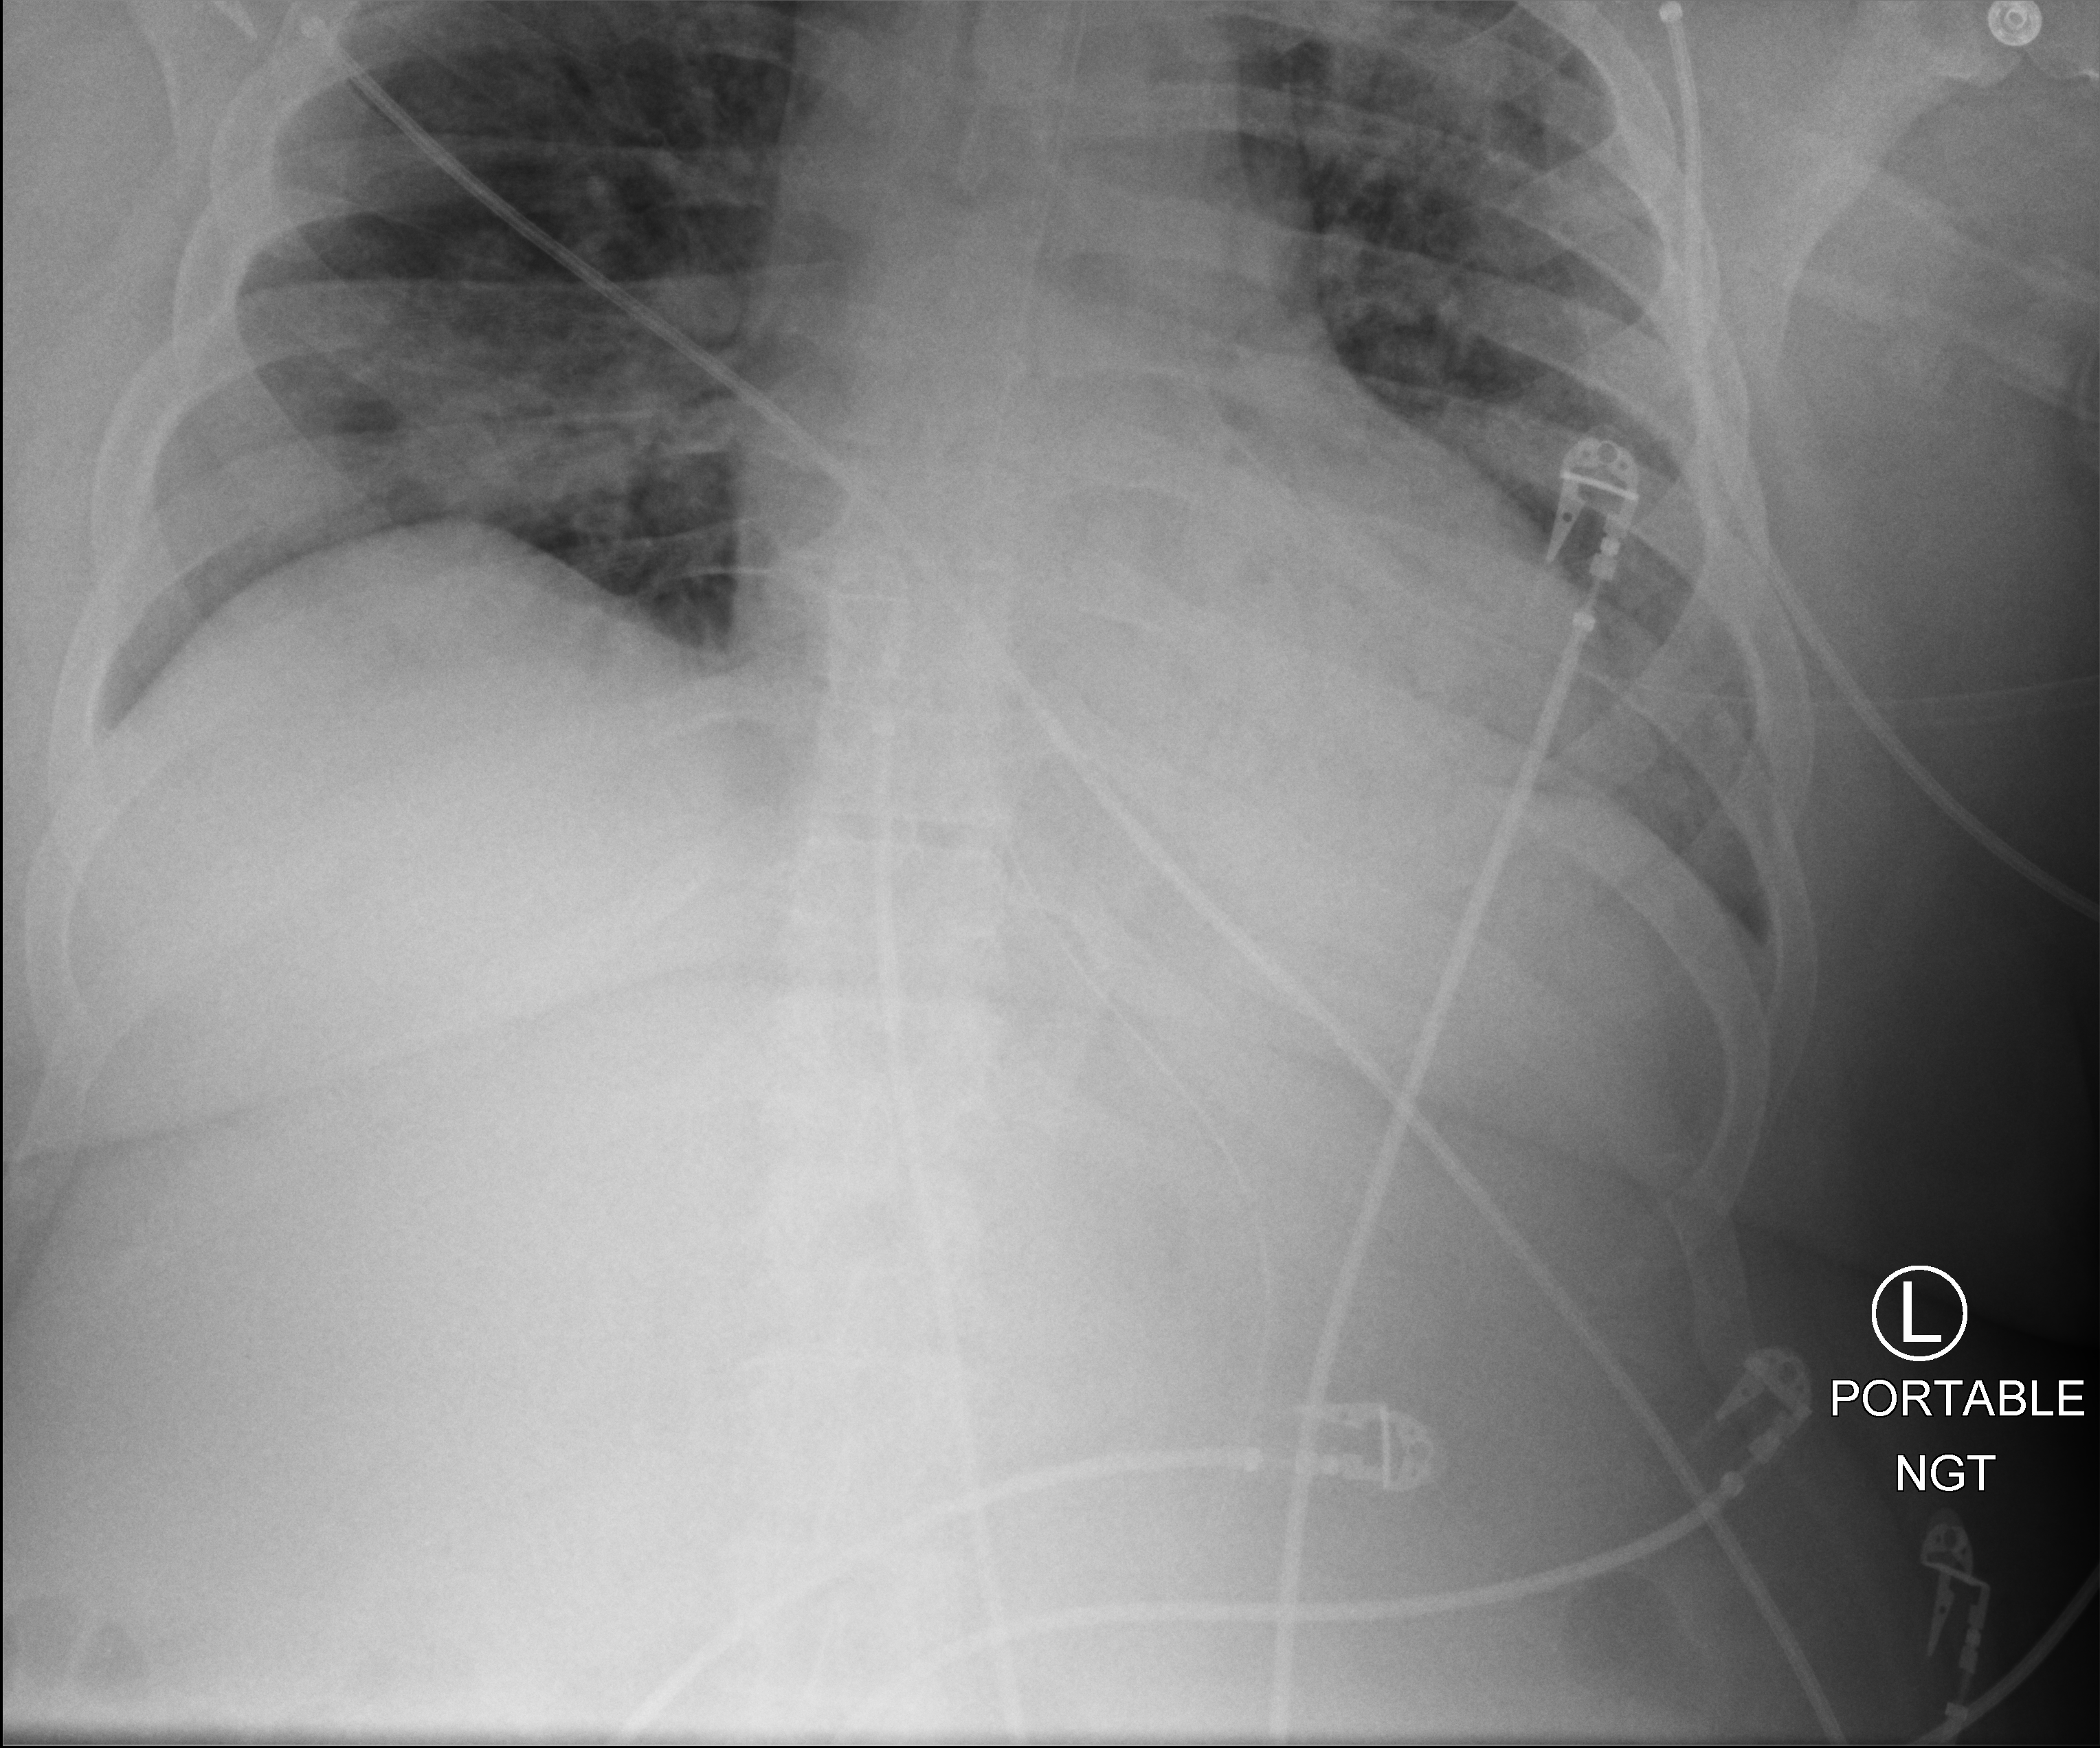
Bedside chest radiograph (computed radiography), anteroposterior (AP) projection. Patient hospitalised with COVID-19, aged 18–59 years.
From the hospital-stay record, not from the radiograph (when in the stay this image was taken is not recorded): admitted to intensive care during this hospital stay: yes.